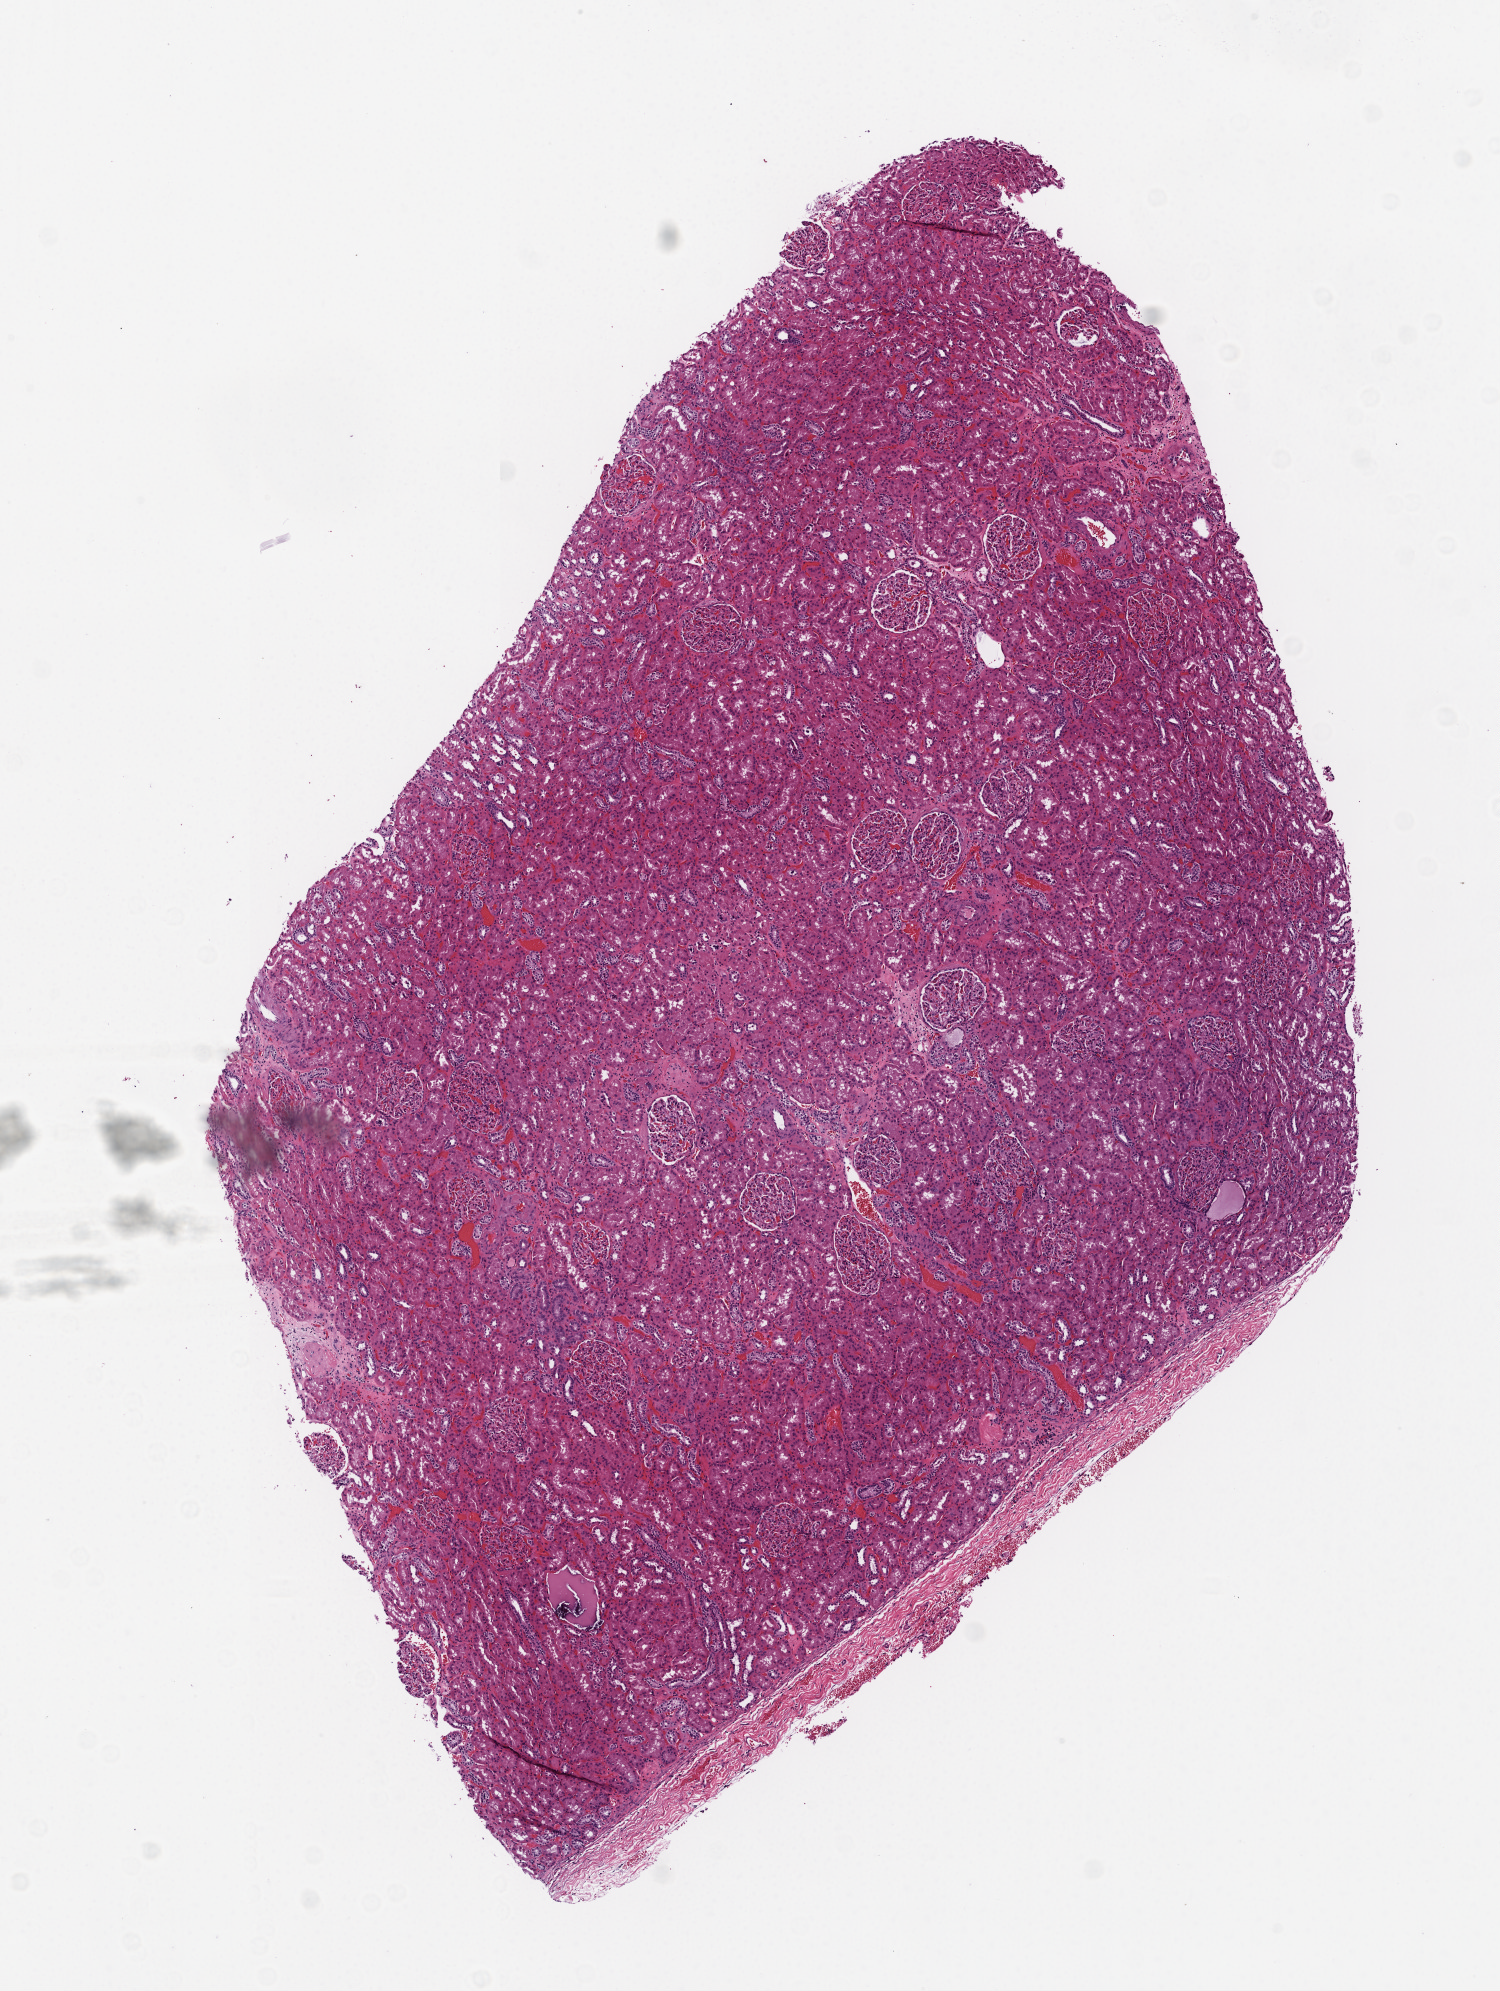
Whole-slide histology image, H&E-stained — whole scanned area (about 6.0 x 8.0 mm) shown as a low-resolution overview. Frozen section from the top of the tissue portion. Solid tissue normal (non-tumour tissue) sample from the kidney. Patient: male, age at initial diagnosis 59 years.
This section: solid tissue normal sample (biorepository sample class). Patient diagnosis: Clear cell adenocarcinoma, NOS.